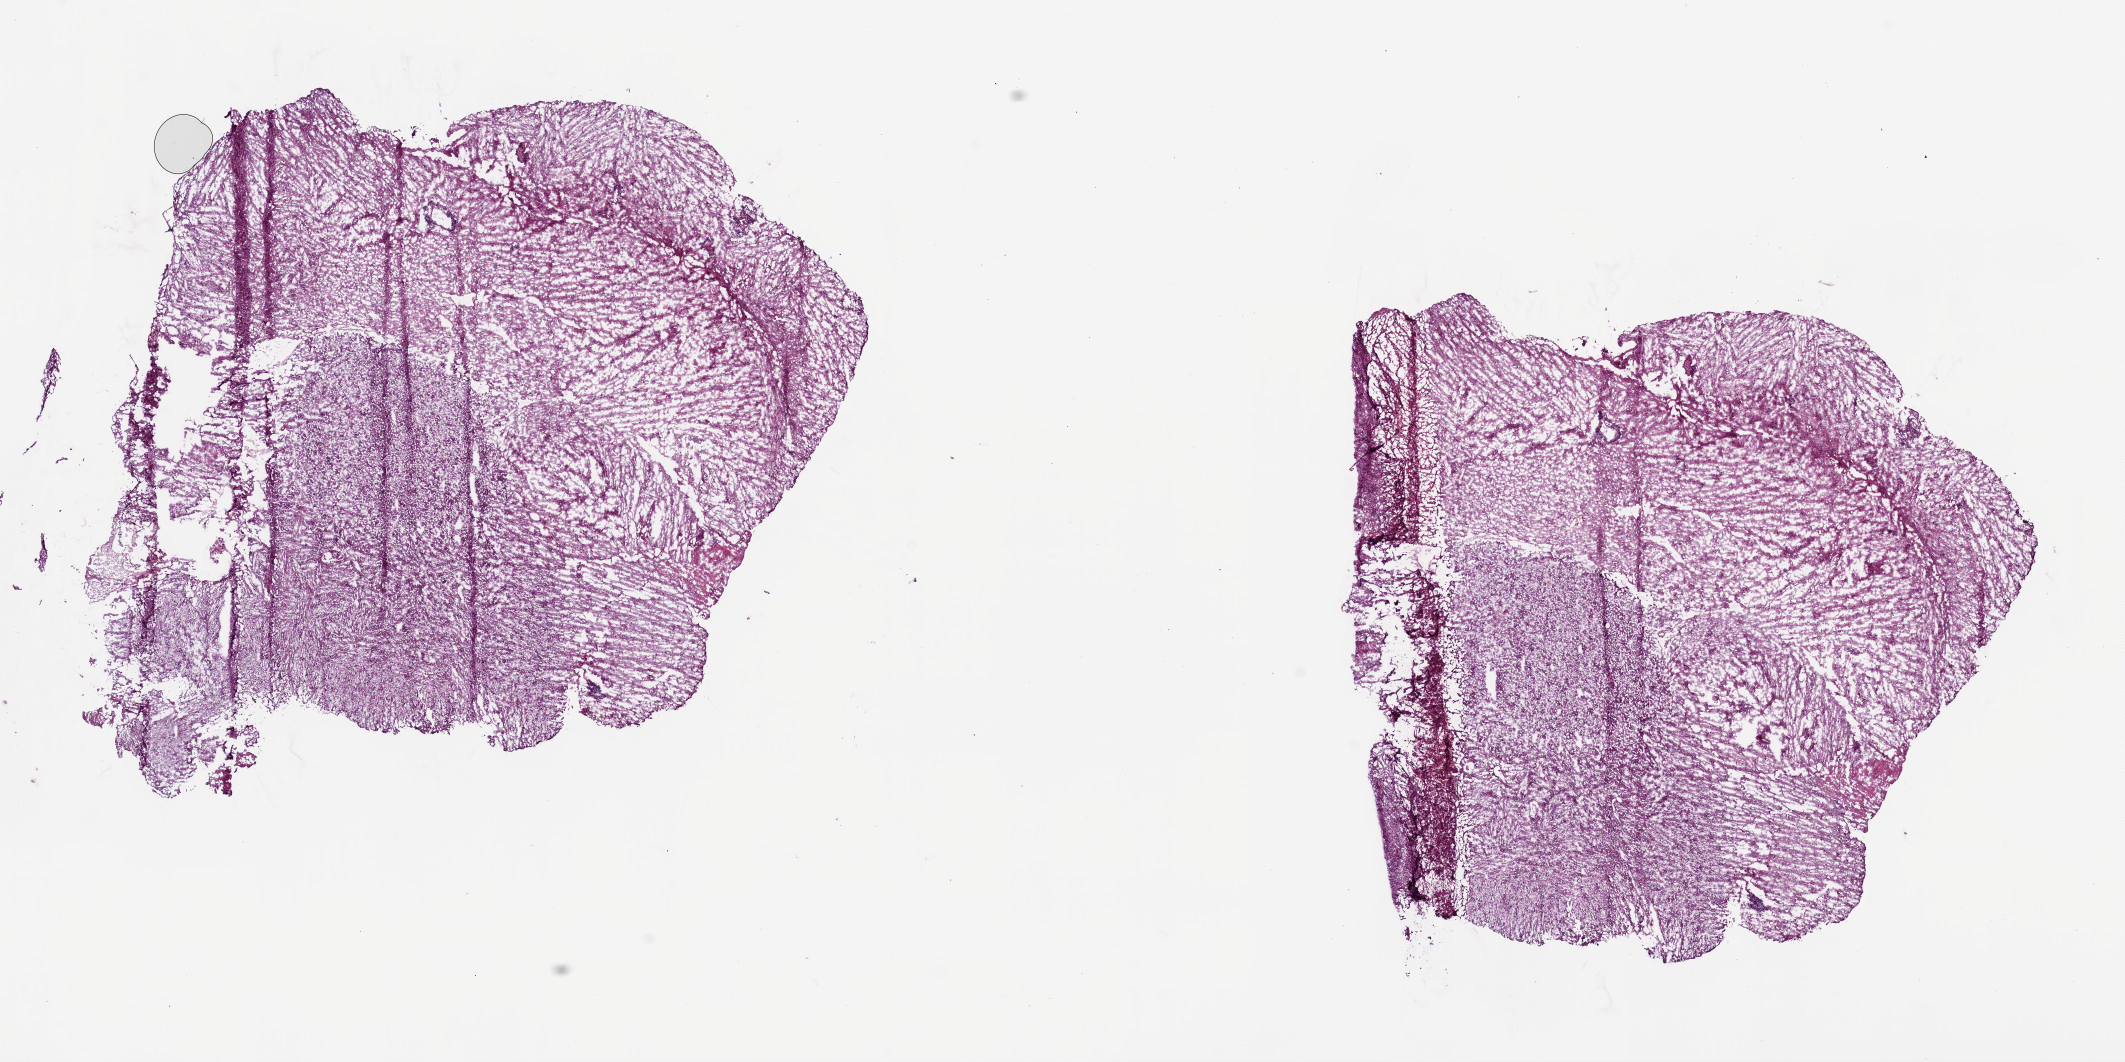
Digitized H&E tissue section (whole slide), low-resolution overview of the scanned area, about 17.1 x 8.5 mm; frozen section from the bottom of the tissue portion; brain, primary tumour sample. Patient: male, age at initial diagnosis 67 years. Histologic grade: G3 (poorly differentiated). Slide review estimates, as recorded: tumour cells 100%, tumour nuclei 75%, normal cells 0%, stromal cells 0%, necrosis 0%.
Laterality: right. Diagnosis: Astrocytoma, anaplastic.